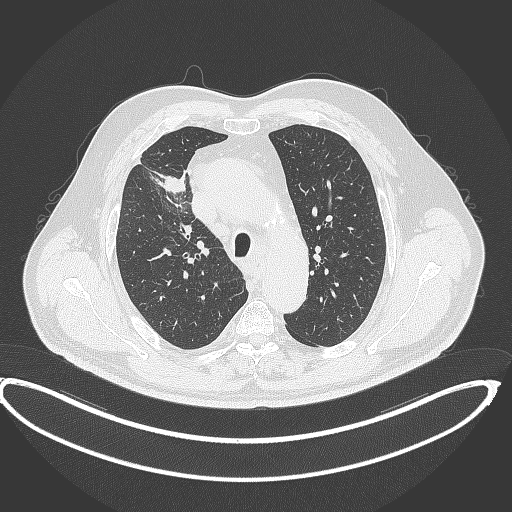
Chest CT, one axial slice. Slice 299 of 390 in the series (ordered by position). Reconstruction kernel B70f. Lung window (W 1500 / L -600 HU). 1 mm slice thickness. 512 × 512 image matrix, field of view 448 × 448 mm. Patient: male, 62 years. Case-level facts recorded for this patient, not image findings: clinical TNM (as recorded): T1c N3 M1c.
Outlined on this slice (rectangle marked by the reading radiologist):
- lung tumour (recorded histology: adenocarcinoma): box from (x=161, y=173) to (x=187, y=196) px